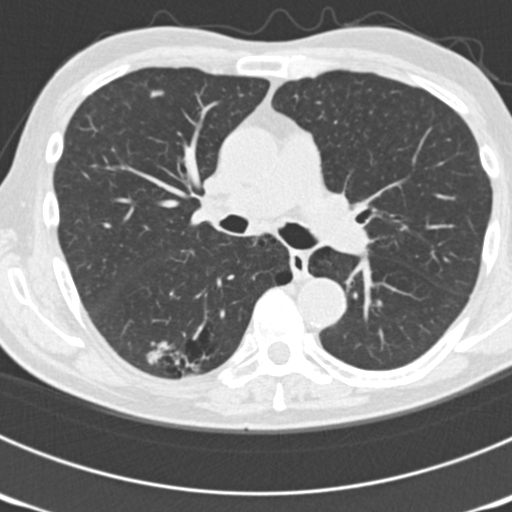
Axial slice from a low-dose chest CT screening exam, third annual screen, lung window (W 1500 / L -600 HU), 2 mm slice thickness. Male participant, aged 70 years at enrolment.
Expert-annotated lung lesion, box from (x=143, y=311) to (x=236, y=386) px. The screening reader recorded 3 non-calcified nodules or masses ≥4 mm on this exam (right upper lobe, left upper lobe, right lower lobe); which of them this box marks is not recorded. Official screen result: positive, other. Later outcome: lung cancer diagnosed 14 days after this screen — bronchiolo-alveolar adenocarcinoma, NOS, right lower lobe, poorly differentiated (G3), stage IB (AJCC 6th edition), 30 mm at pathology.